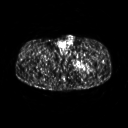
FDG PET of an extremity soft-tissue mass (from a PET/CT study), one axial slice. Position 261 of 267 along the scan axis. 3.27 mm slice thickness. 128 × 128 image matrix, field of view 500 × 500 mm. Male patient, age 27 years. From the clinical record (not read from this slice): histological type: extraskeletal osteosarcoma; grade: high; site of the primary tumour: left adductur.
Outlined on this slice (expert contour drawn on MRI and transferred to this co-registered scan by the dataset authors):
- gross tumour volume (mass): bounding box (x1, y1, x2, y2) in pixels: (71, 51, 97, 75)